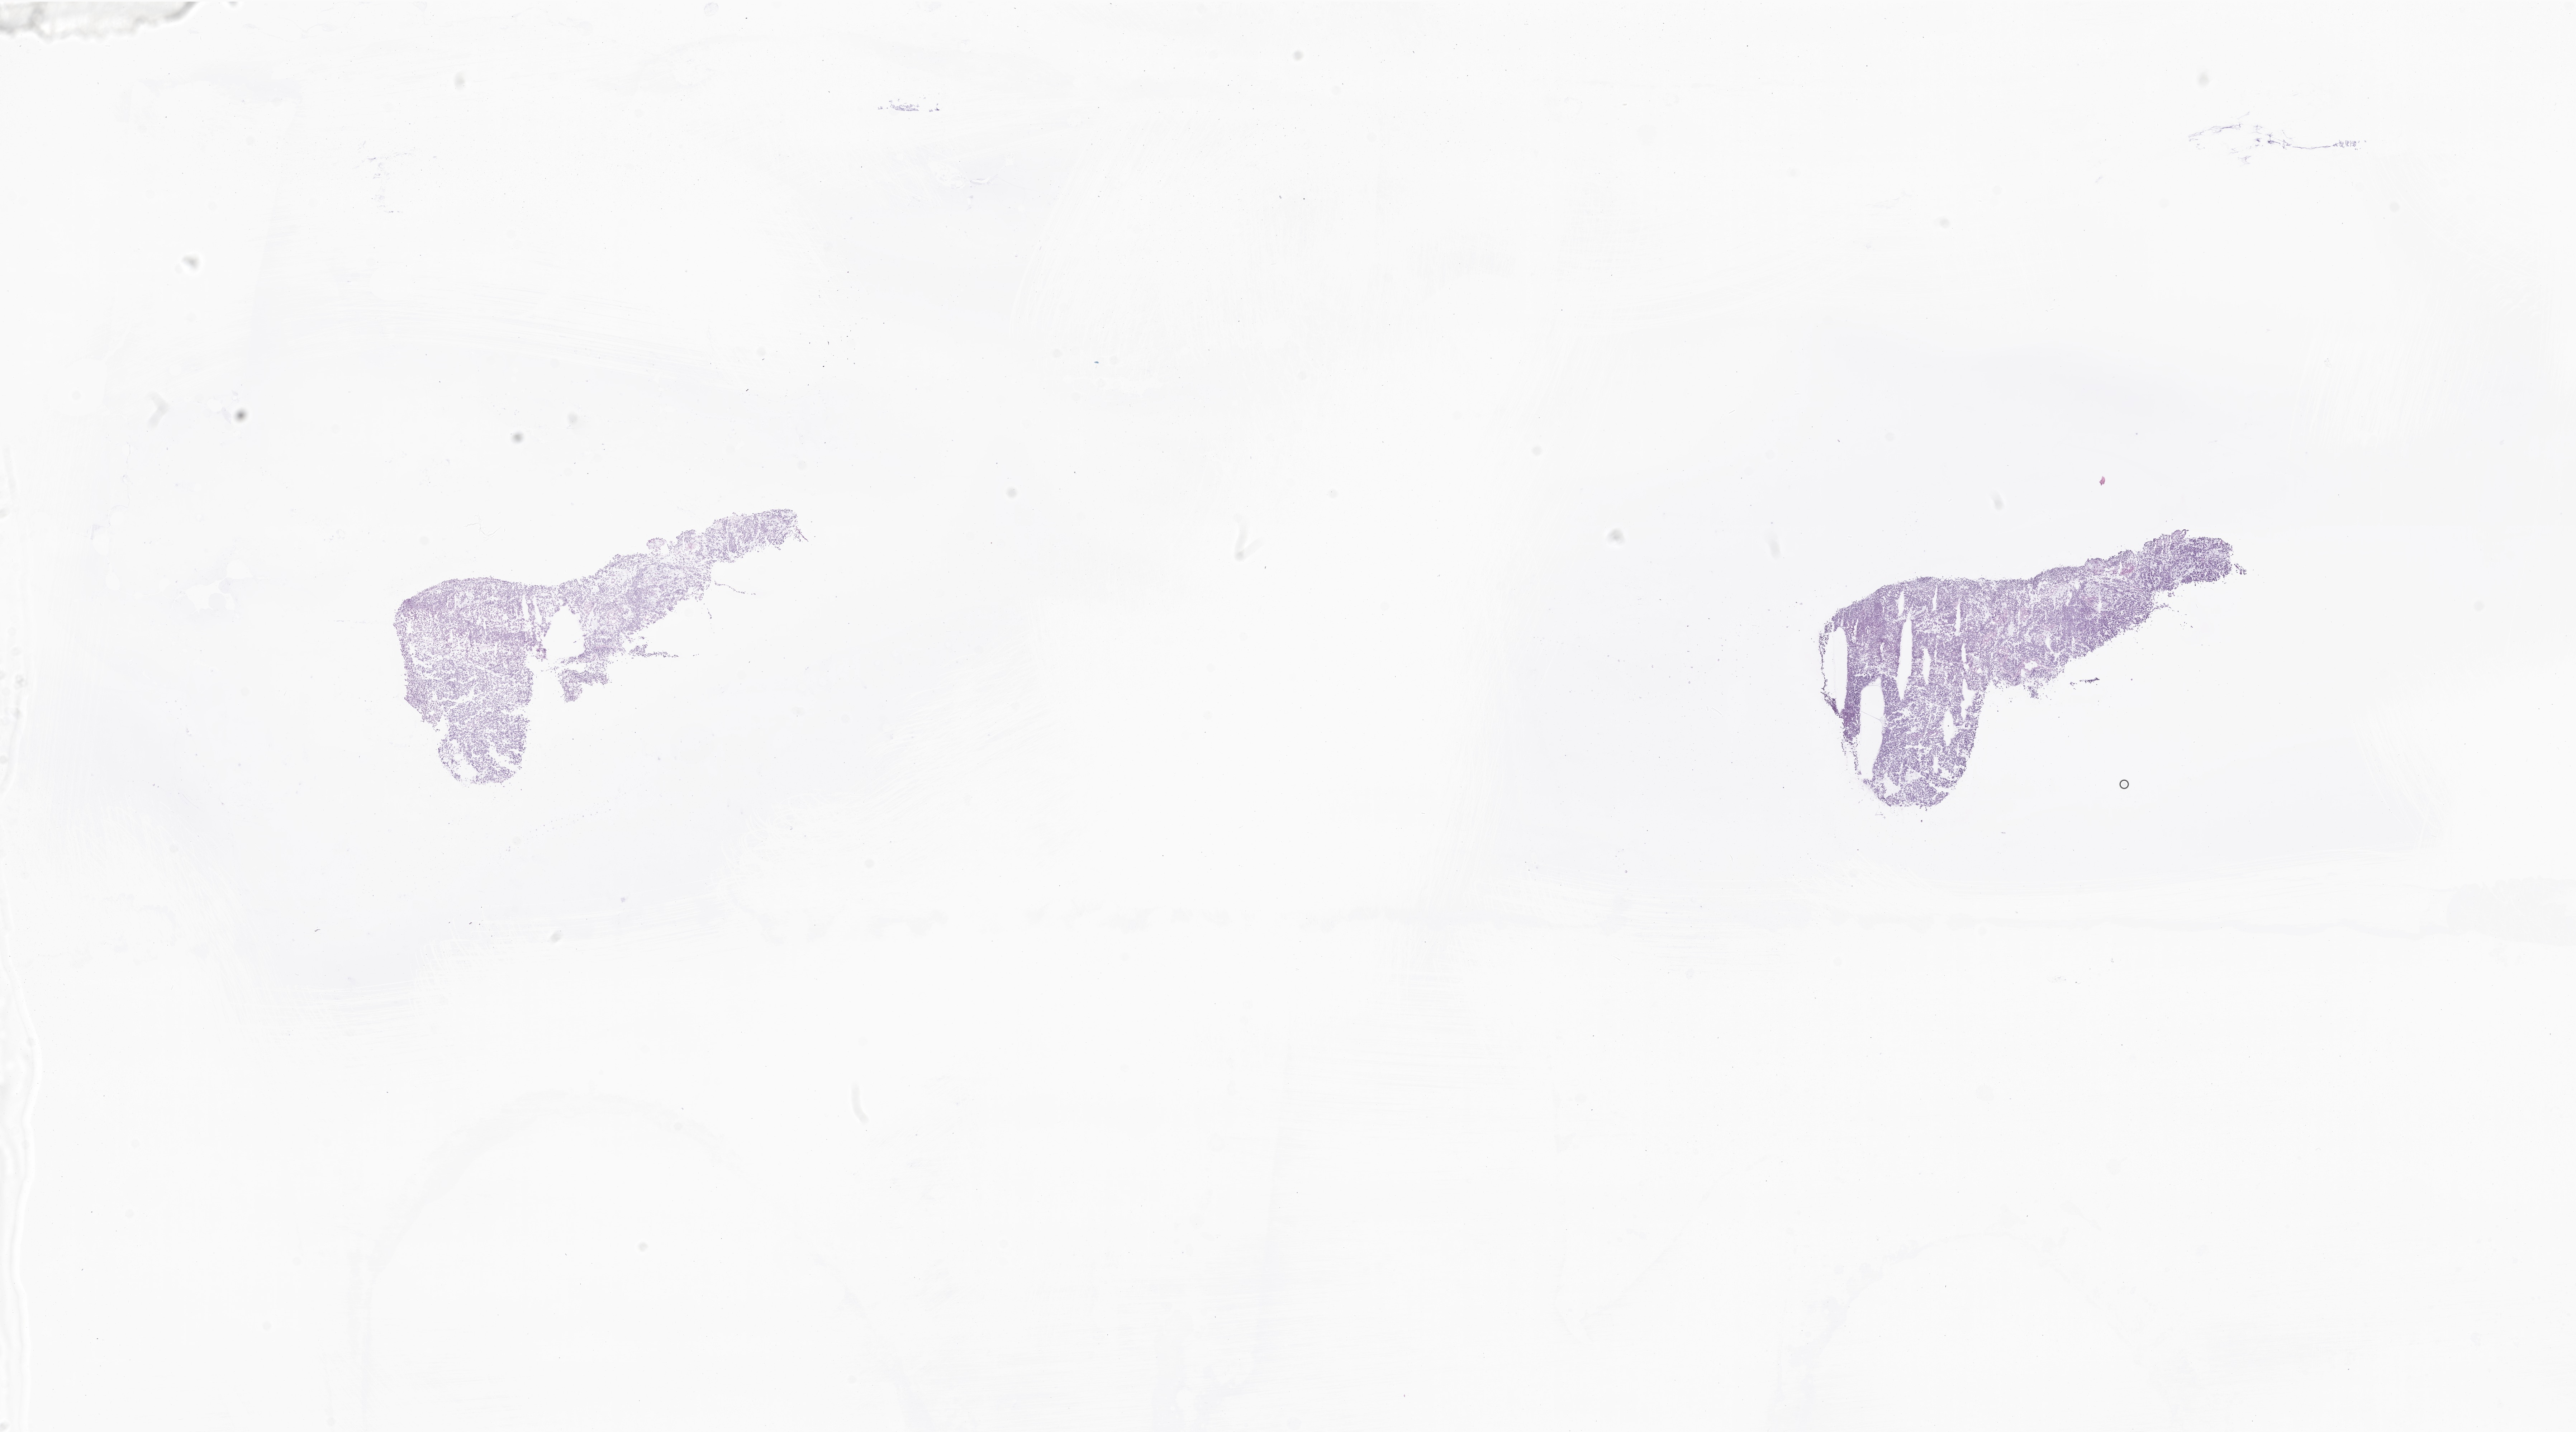
Whole-slide image, H&E stain of tumor tissue from the brain — a low-resolution overview of the entire scanned area, about 30.3 x 16.8 mm; frozen section. Male patient, age 41 months (3 years 5 months).
- recorded diagnosis: Neoplasm, malignant